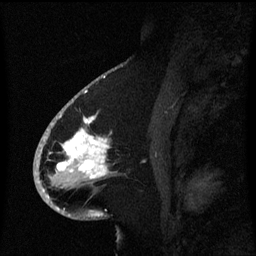
Breast MRI (dynamic contrast-enhanced), one sagittal slice. Position 33 of 60 along the scan axis. Dynamic contrast-enhanced series, image 2 of 3 at this slice position (ordered by acquisition). 1.5 T. TE 4.2 ms, TR 8.4 ms. 256 × 256 image matrix, field of view 200 × 200 mm. Patient: female, 53 years. From the clinical record (not read from this slice): setting: breast cancer imaged before/during neoadjuvant chemotherapy; receptor status: HR-positive, HER2-negative.
Annotated regions visible in this slice (semi-automatic segmentation, software-assisted and operator-edited):
- analysis volume of interest (the breast-tissue region the enhancement analysis was run in; not a lesion): bounding box (x1, y1, x2, y2) in pixels: (49, 108, 119, 201)
- tumour enhancement mask (voxels above the 70 % enhancement threshold inside the analysis volume of interest): (58, 114, 109, 179)